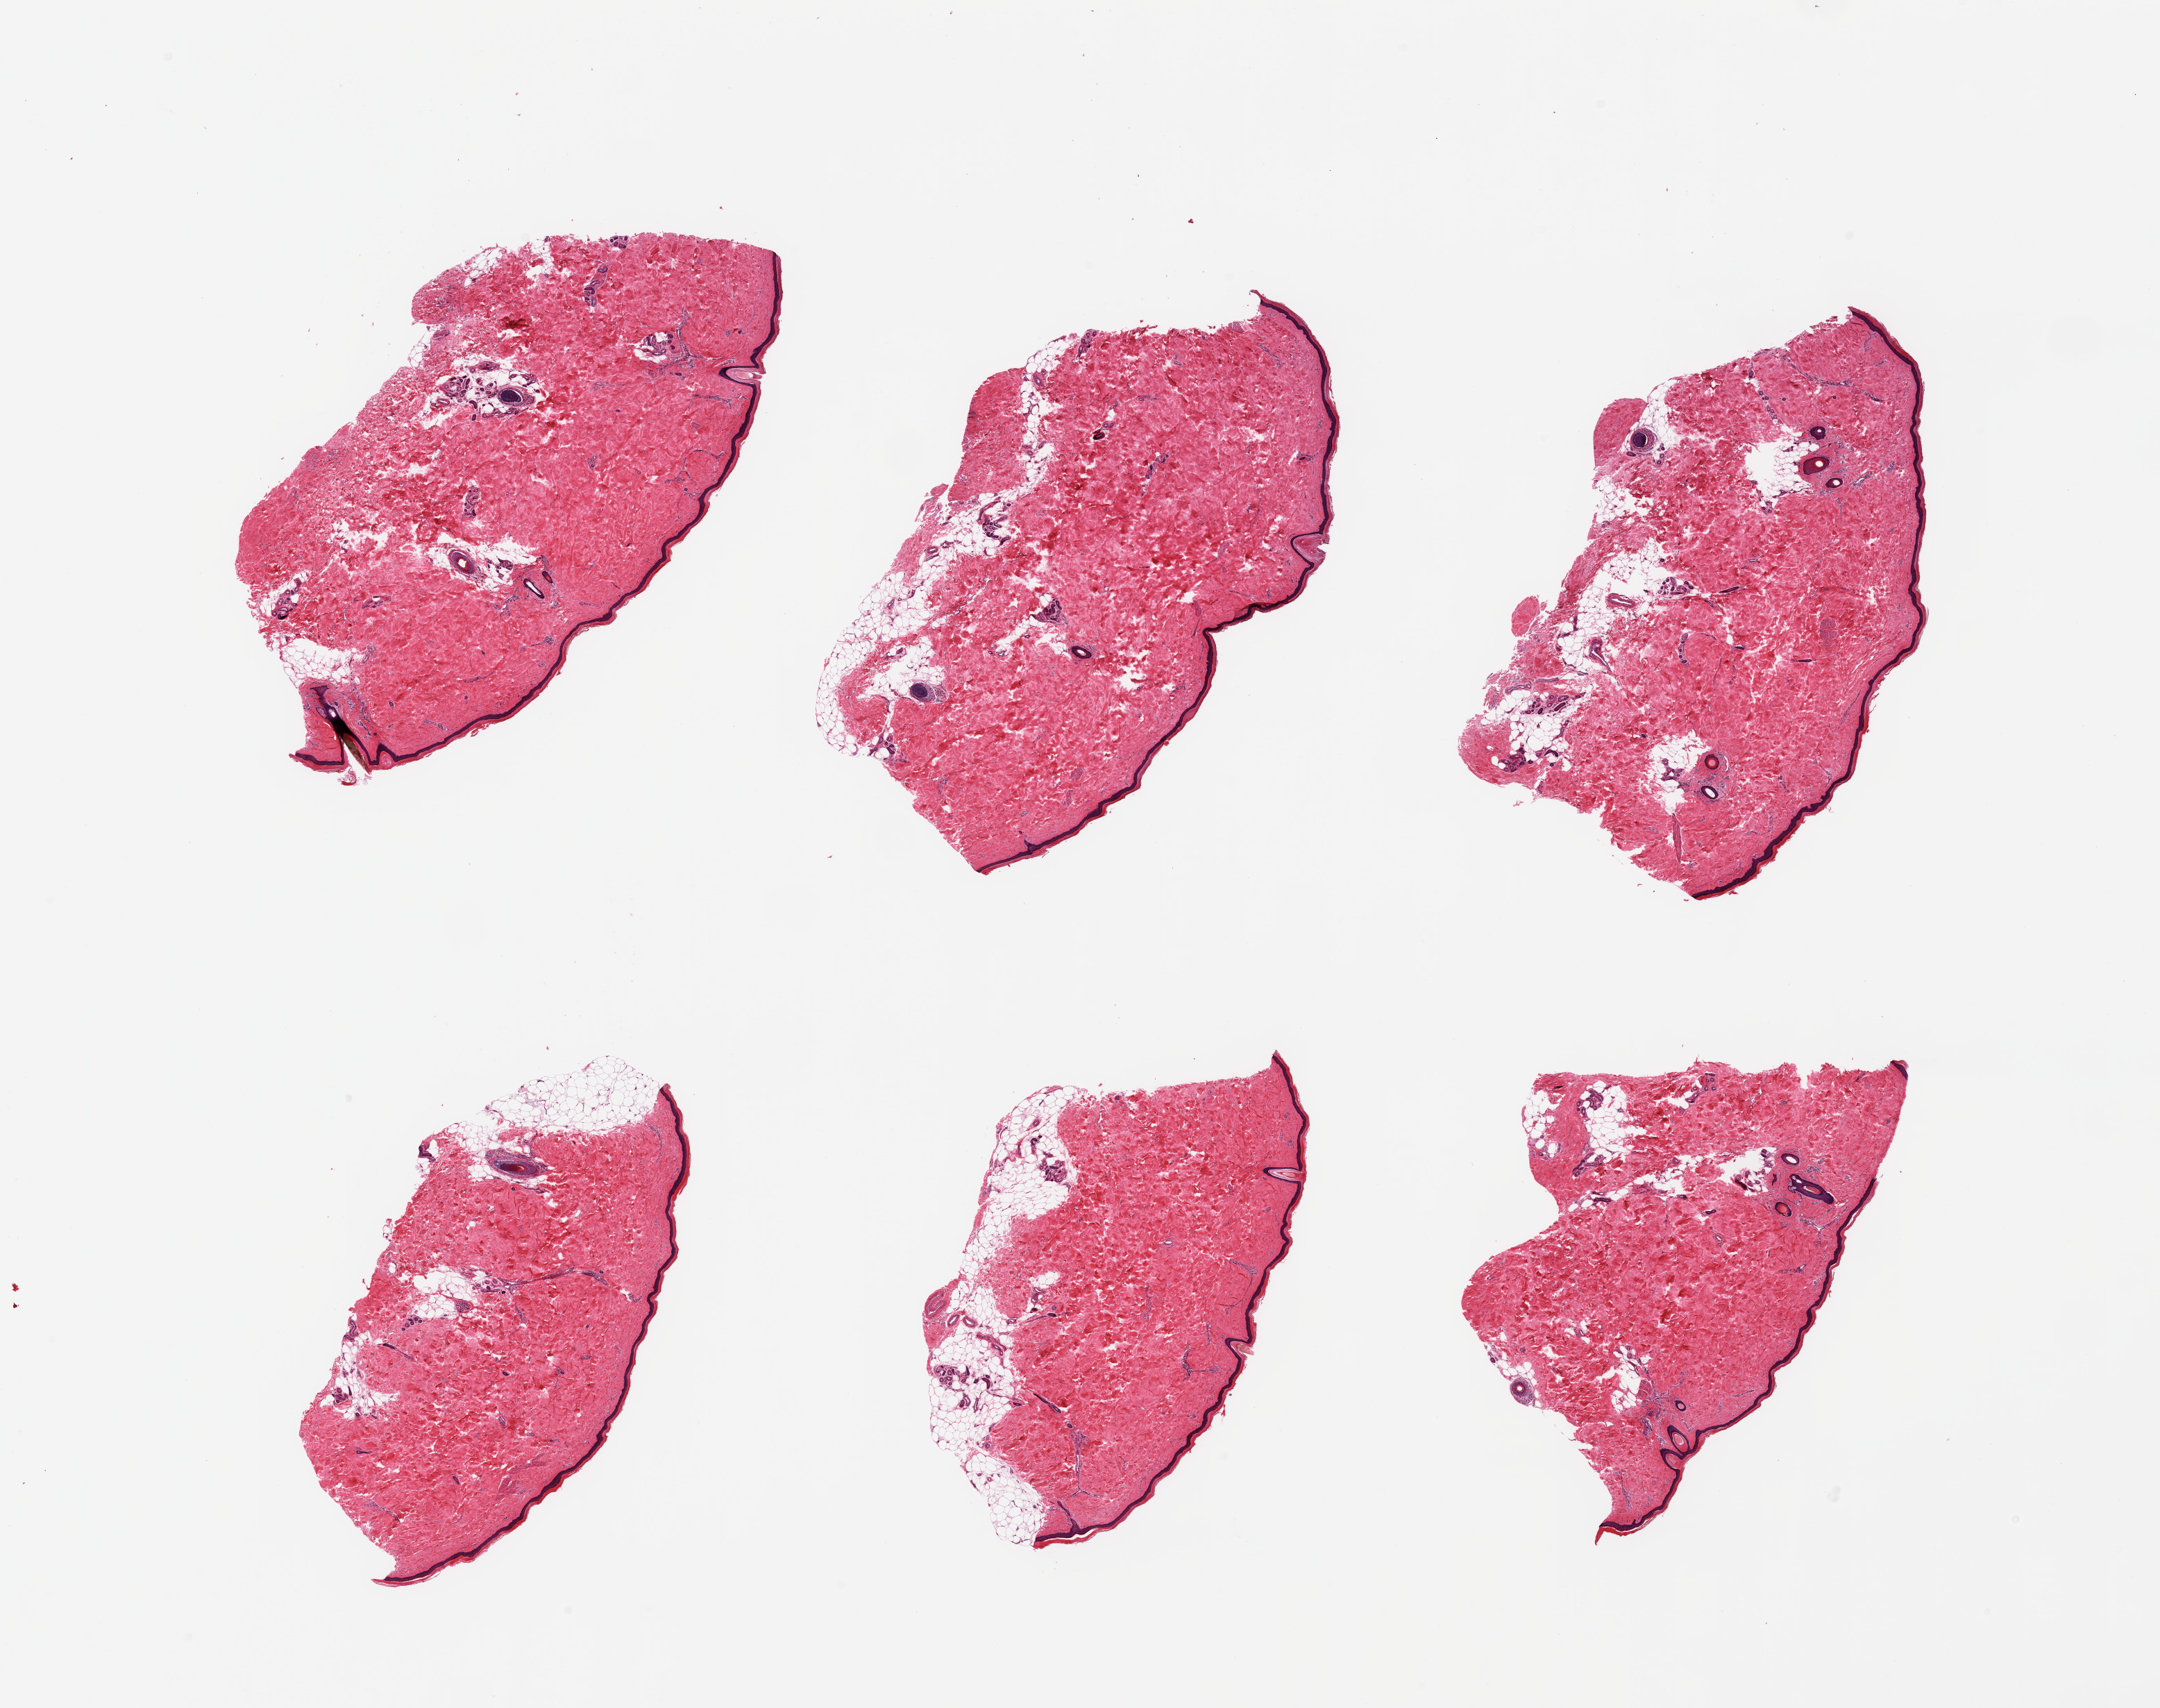
Digitized hematoxylin and eosin (H&E)-stained section, shown as a low-resolution overview of the whole scanned area (about 24.6 x 19.5 mm, acquisition: 20x scan), PAXgene-fixed, paraffin-embedded tissue, target tissue: skin of lower leg, tissue donor sample.
Pathologist's review note for this sample: 6 pieces, moderate dermal fat, focally adherent up to ~0.8mm; squamous epithelium is ~35-40 microns.